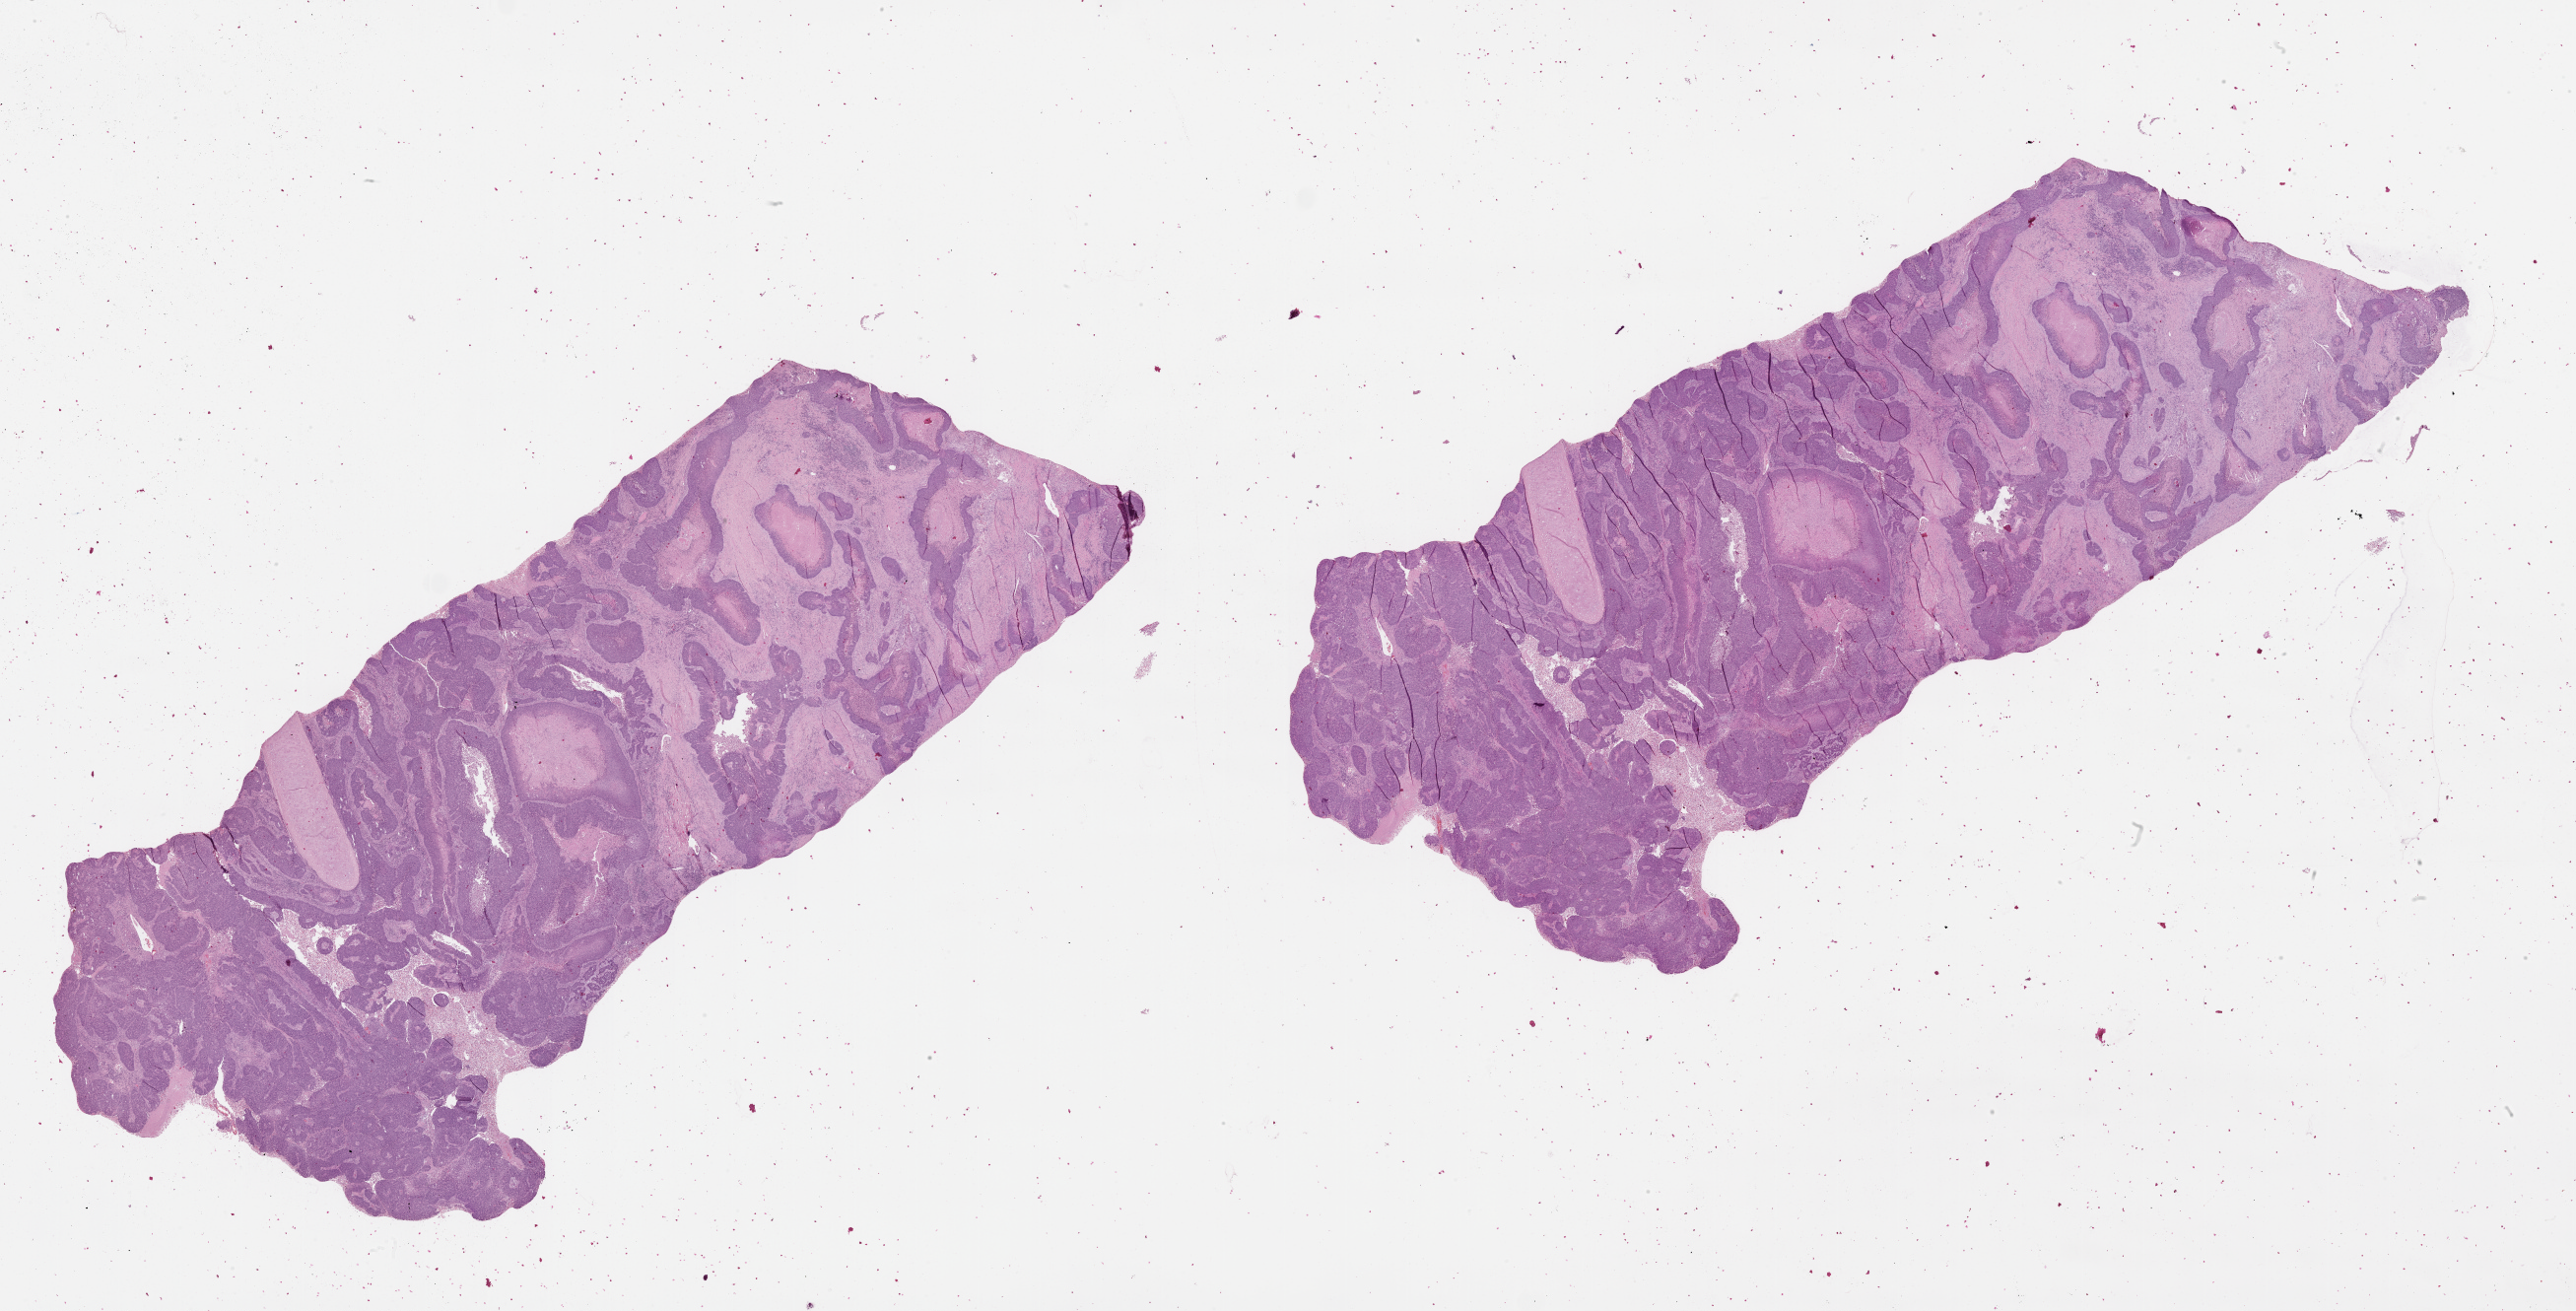
Digitized H&E-stained tissue section (whole slide), whole scanned area (about 42.1 x 21.4 mm, slide scanned at 20x) shown as a low-resolution overview; lung, tumour tissue. Patient: male, age 69 years.
Patient diagnosis (cohort enrolment): squamous cell carcinoma (lung).